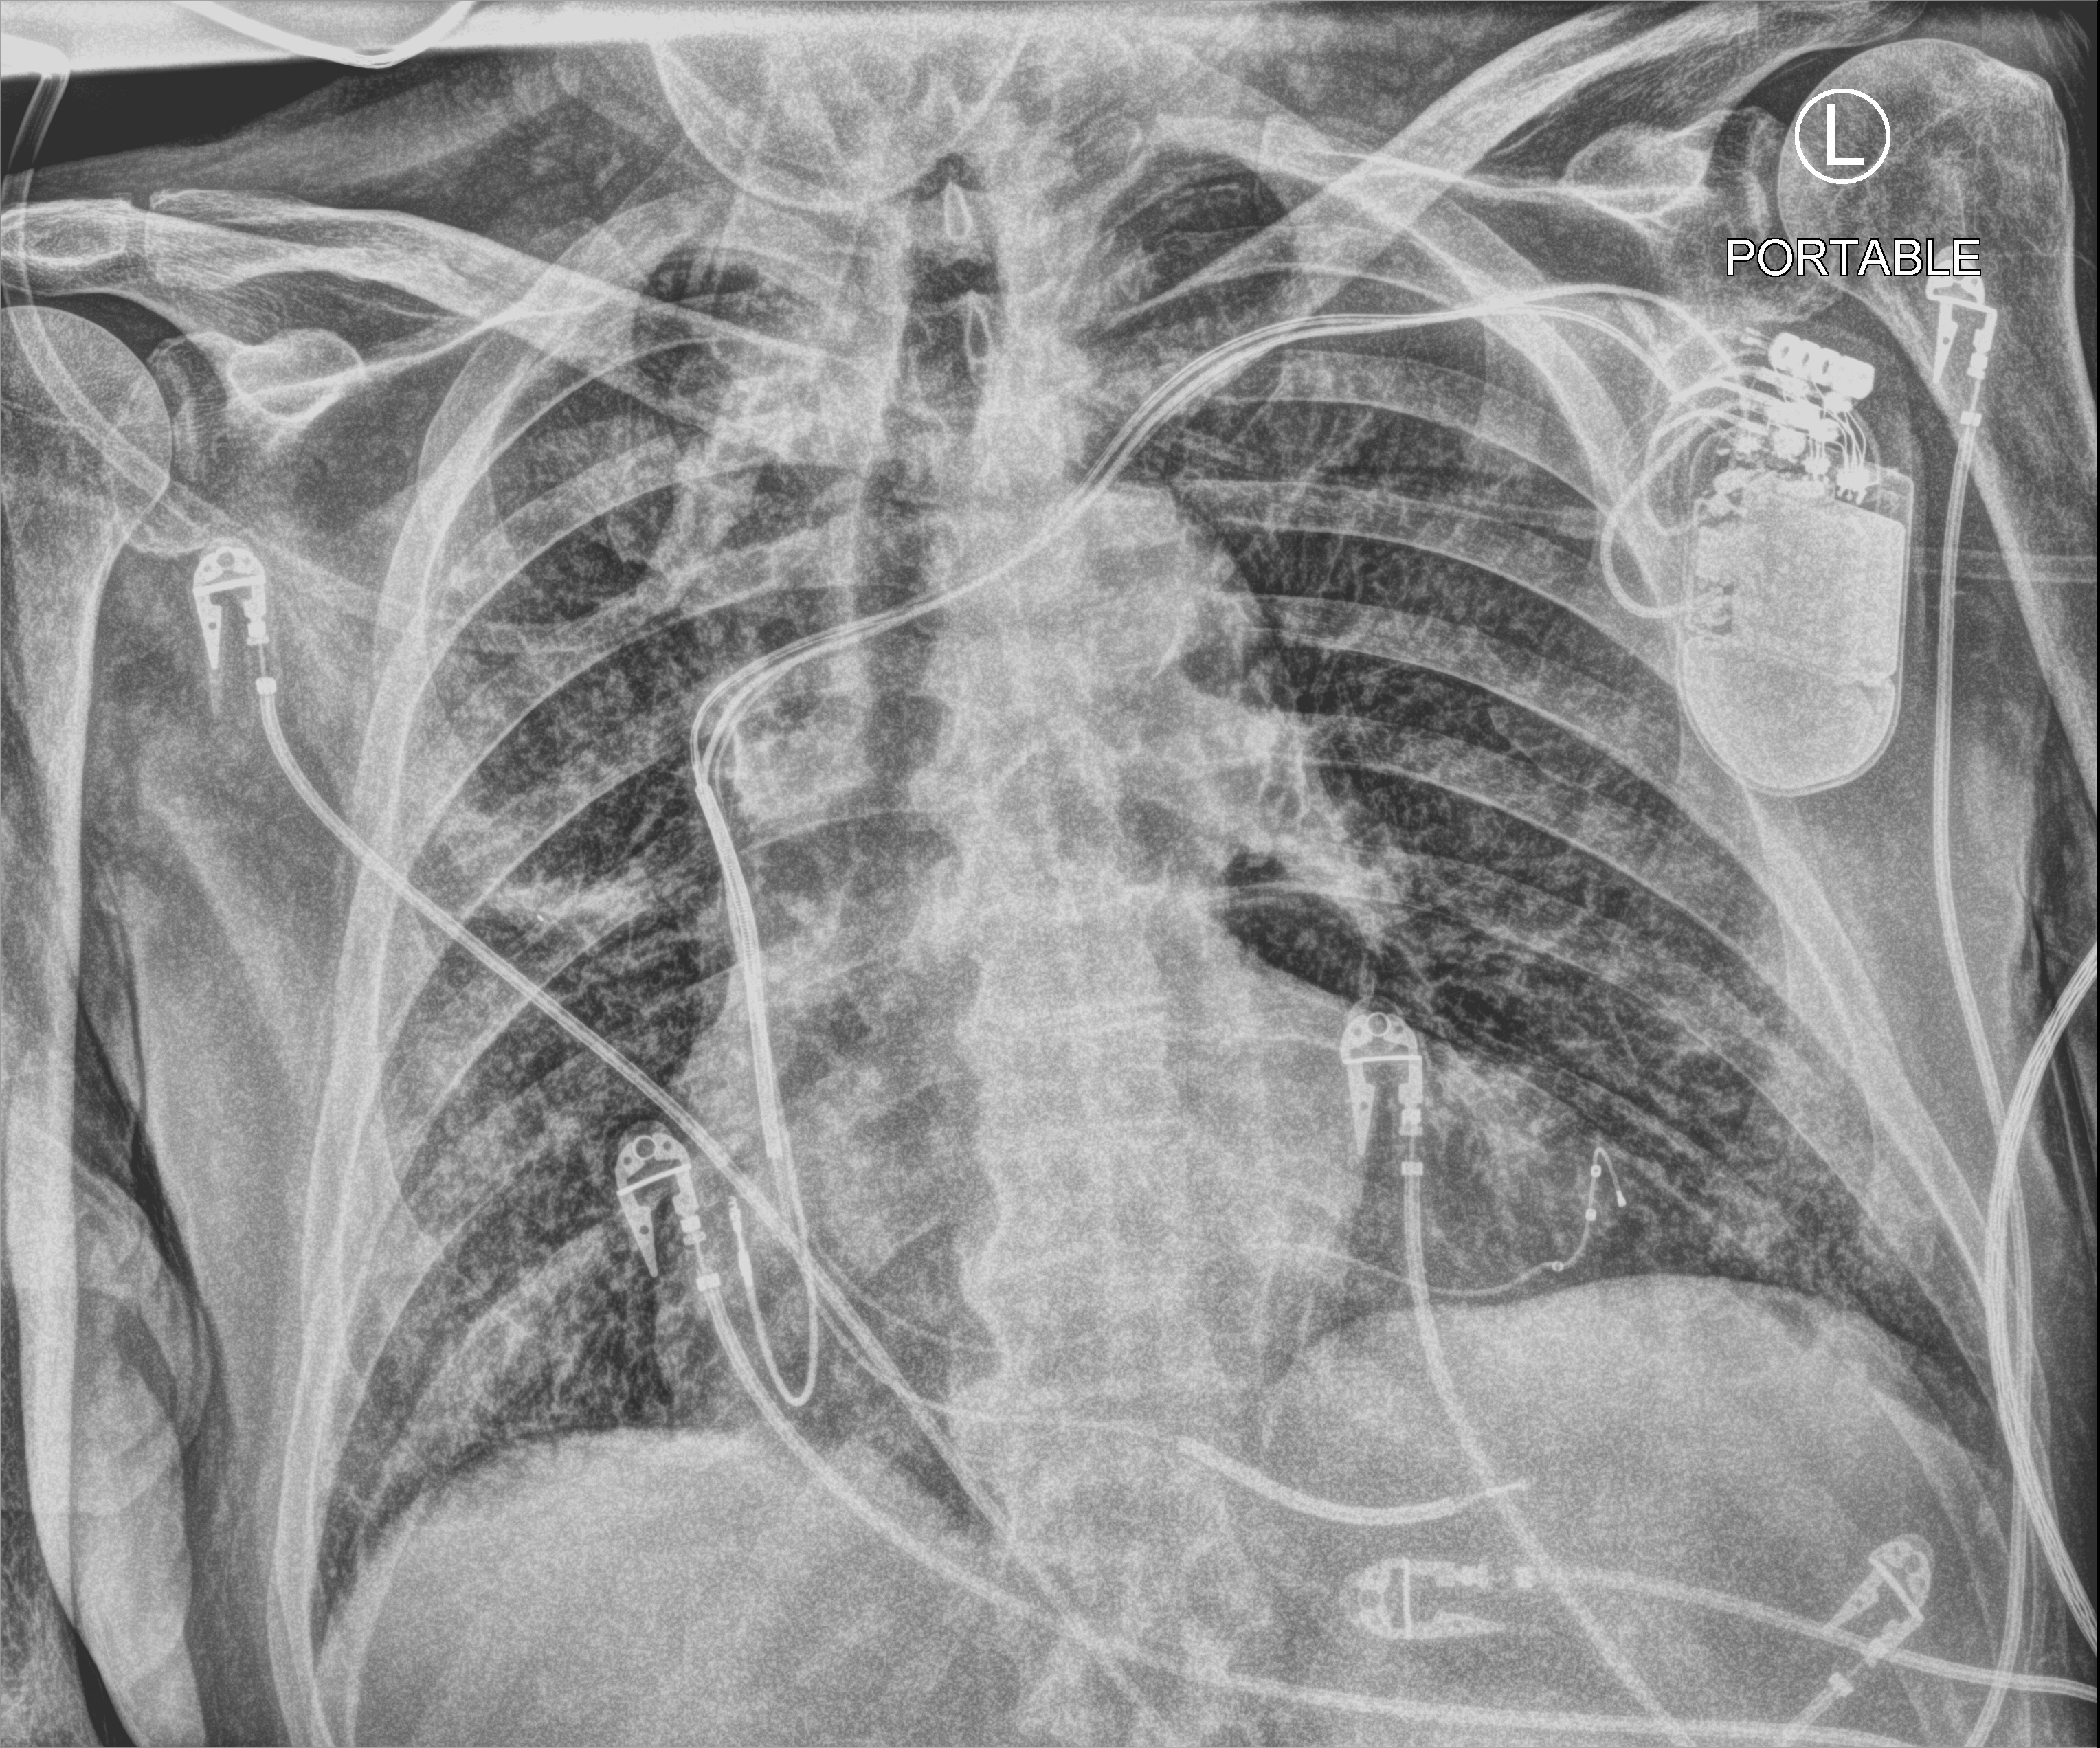
Chest X-ray (portable); anteroposterior (AP) projection. Male patient hospitalised with COVID-19, age 75–90 years.
Hospital-stay facts (about this admission, not read from this image; timing relative to this image not recorded):
- mechanically ventilated during this hospital stay: no
- admitted to intensive care during this hospital stay: no